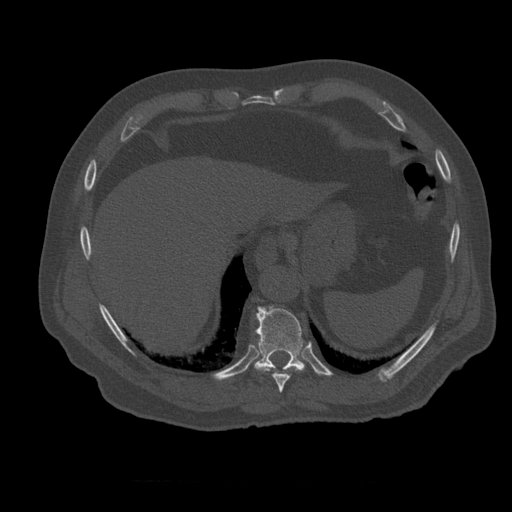
CT including the spine, one axial slice; position 308 of 399 along the scan axis; 120 kVp; bone window (W 1800 / L 400 HU); 1.25 mm slice thickness; 512 × 512 image matrix. Patient age 73 years. Case-level facts recorded for this patient, not image findings: primary cancer: prostate; vertebrae with lytic lesions (as recorded): L2.
Annotated regions visible in this slice (semi-automatically segmented with operator editing):
- T10 vertebra: bounding box (x1, y1, x2, y2) in pixels: (255, 306, 318, 374)
- T12 vertebra: (268, 348, 278, 358)
- T9 vertebra: (259, 367, 304, 393)